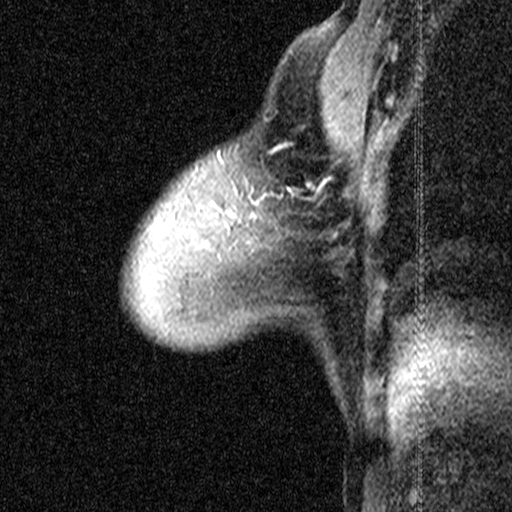
Breast MRI (dynamic contrast-enhanced), one sagittal slice; position 32 of 44 along the scan axis; dynamic contrast-enhanced study with each time point stored as its own series, time point 2 of 3 at this slice position (early post-contrast, ordered by acquisition time); 1.5 T; TE 4.5 ms, TR 11 ms; 3 mm slice thickness; 512 × 512 image matrix, field of view 200 × 200 mm. Female patient, age 53 years. From the clinical record (not read from this slice): setting: breast cancer imaged before/during neoadjuvant chemotherapy; receptor status: HR-positive, HER2-negative.
Outlined on this slice (semi-automatic segmentation, software-assisted and operator-edited):
- analysis volume of interest (the breast-tissue region the enhancement analysis was run in; not a lesion): bounding box [x1, y1, x2, y2] px = [198, 152, 299, 267]
- tumour enhancement mask (voxels above the 90 % enhancement threshold inside the analysis volume of interest): [287, 187, 289, 190]